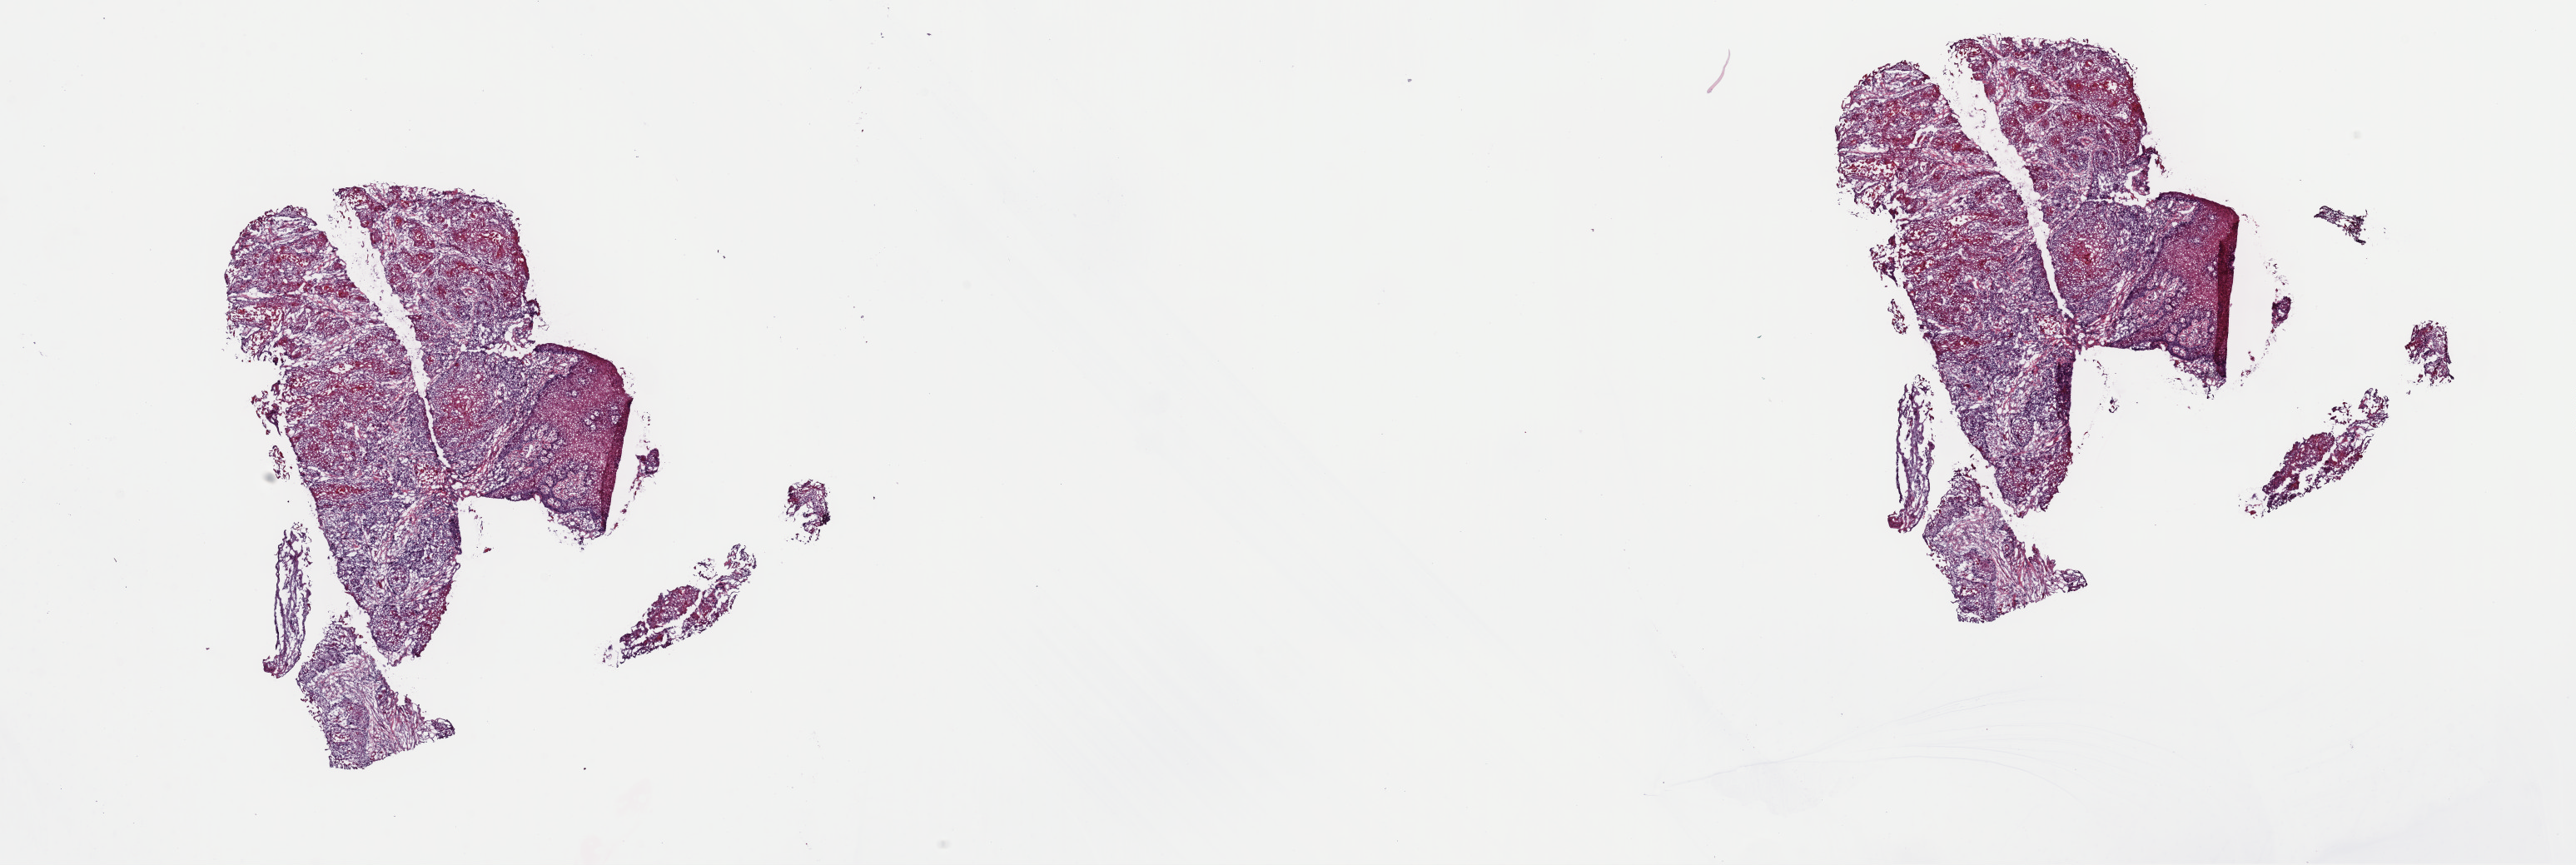
Whole-slide histology image, H&E-stained, whole scanned area (about 24.4 x 8.2 mm) shown as a low-resolution overview, frozen section, sample: primary tumour, head and neck. Patient: male, age at initial diagnosis 46 years. Histologic grade: G1 (well differentiated). Composition of this section per pathologist review: tumour cells 70%, tumour nuclei 70%, normal cells 0%, stromal cells 30%, necrosis 0%. Infiltration values recorded for this section: lymphocyte infiltration 3%, monocyte infiltration 0%, neutrophil infiltration 0%.
* TNM: T2 N1 M0
* AJCC pathologic stage: III (4th edition)
* pathologic diagnosis: Squamous cell carcinoma, keratinizing, NOS (tongue, NOS)
* lymph nodes positive (case pathology): 1 of 26 examined